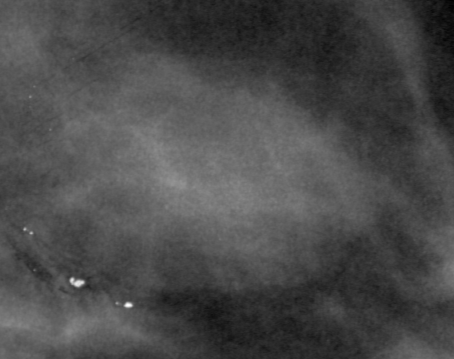
Region of interest cut from a scanned film mammogram (one marked finding); right breast; CC view.
Finding: mass, shape oval, margins obscured; BI-RADS assessment category 3; pathology (as recorded): benign.